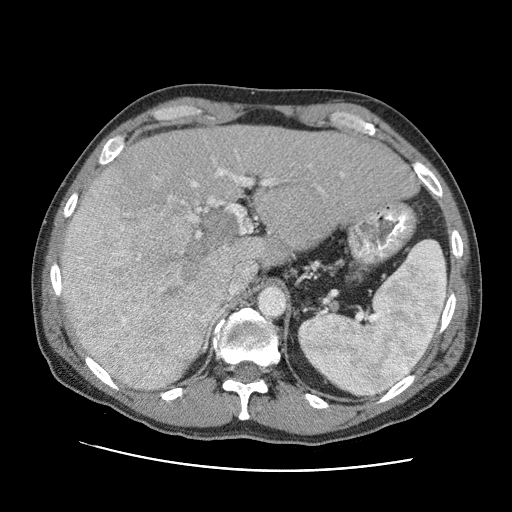
Contrast-enhanced abdominal CT (liver protocol), one axial slice; position 59 of 95 along the scan axis; reconstruction kernel STANDARD; one of 2 acquisitions stored at this slice position; soft-tissue window (W 400 / L 40 HU); 512 × 512 image matrix, field of view 360 × 360 mm. Case-level facts recorded for this patient, not image findings: diagnosis: hepatocellular carcinoma (patient treated with transarterial chemoembolisation; whether this scan precedes or follows treatment is not stated here); TNM stage (as recorded): Stage-IVA; Child-Pugh class: A; tumour nodularity: multinodular.
Outlined on this slice (semi-automatically segmented with operator editing):
- liver parenchyma outside the tumour (the mass and vessels are separate outlines, so this box may not span the whole liver): bounding box [x1, y1, x2, y2] px = [62, 124, 418, 390]
- mass: [61, 144, 244, 386]
- liver vessels: [169, 156, 344, 276]